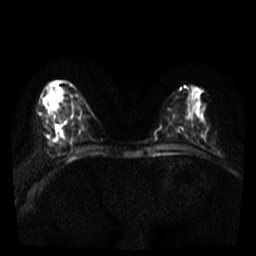
Breast MRI, one axial slice; position 12 of 36 along the scan axis; diffusion-weighted series; image 2 of 4 stored at this slice position (different b-values; order by instance number); 3 T; 5 mm slice thickness; 256 × 256 image matrix, field of view 300 × 300 mm. Female patient.
Structures marked on this image (expert manual segmentation):
- tumour on diffusion-weighted imaging: bounding box <51,102,60,131> (left, top, right, bottom; pixels)